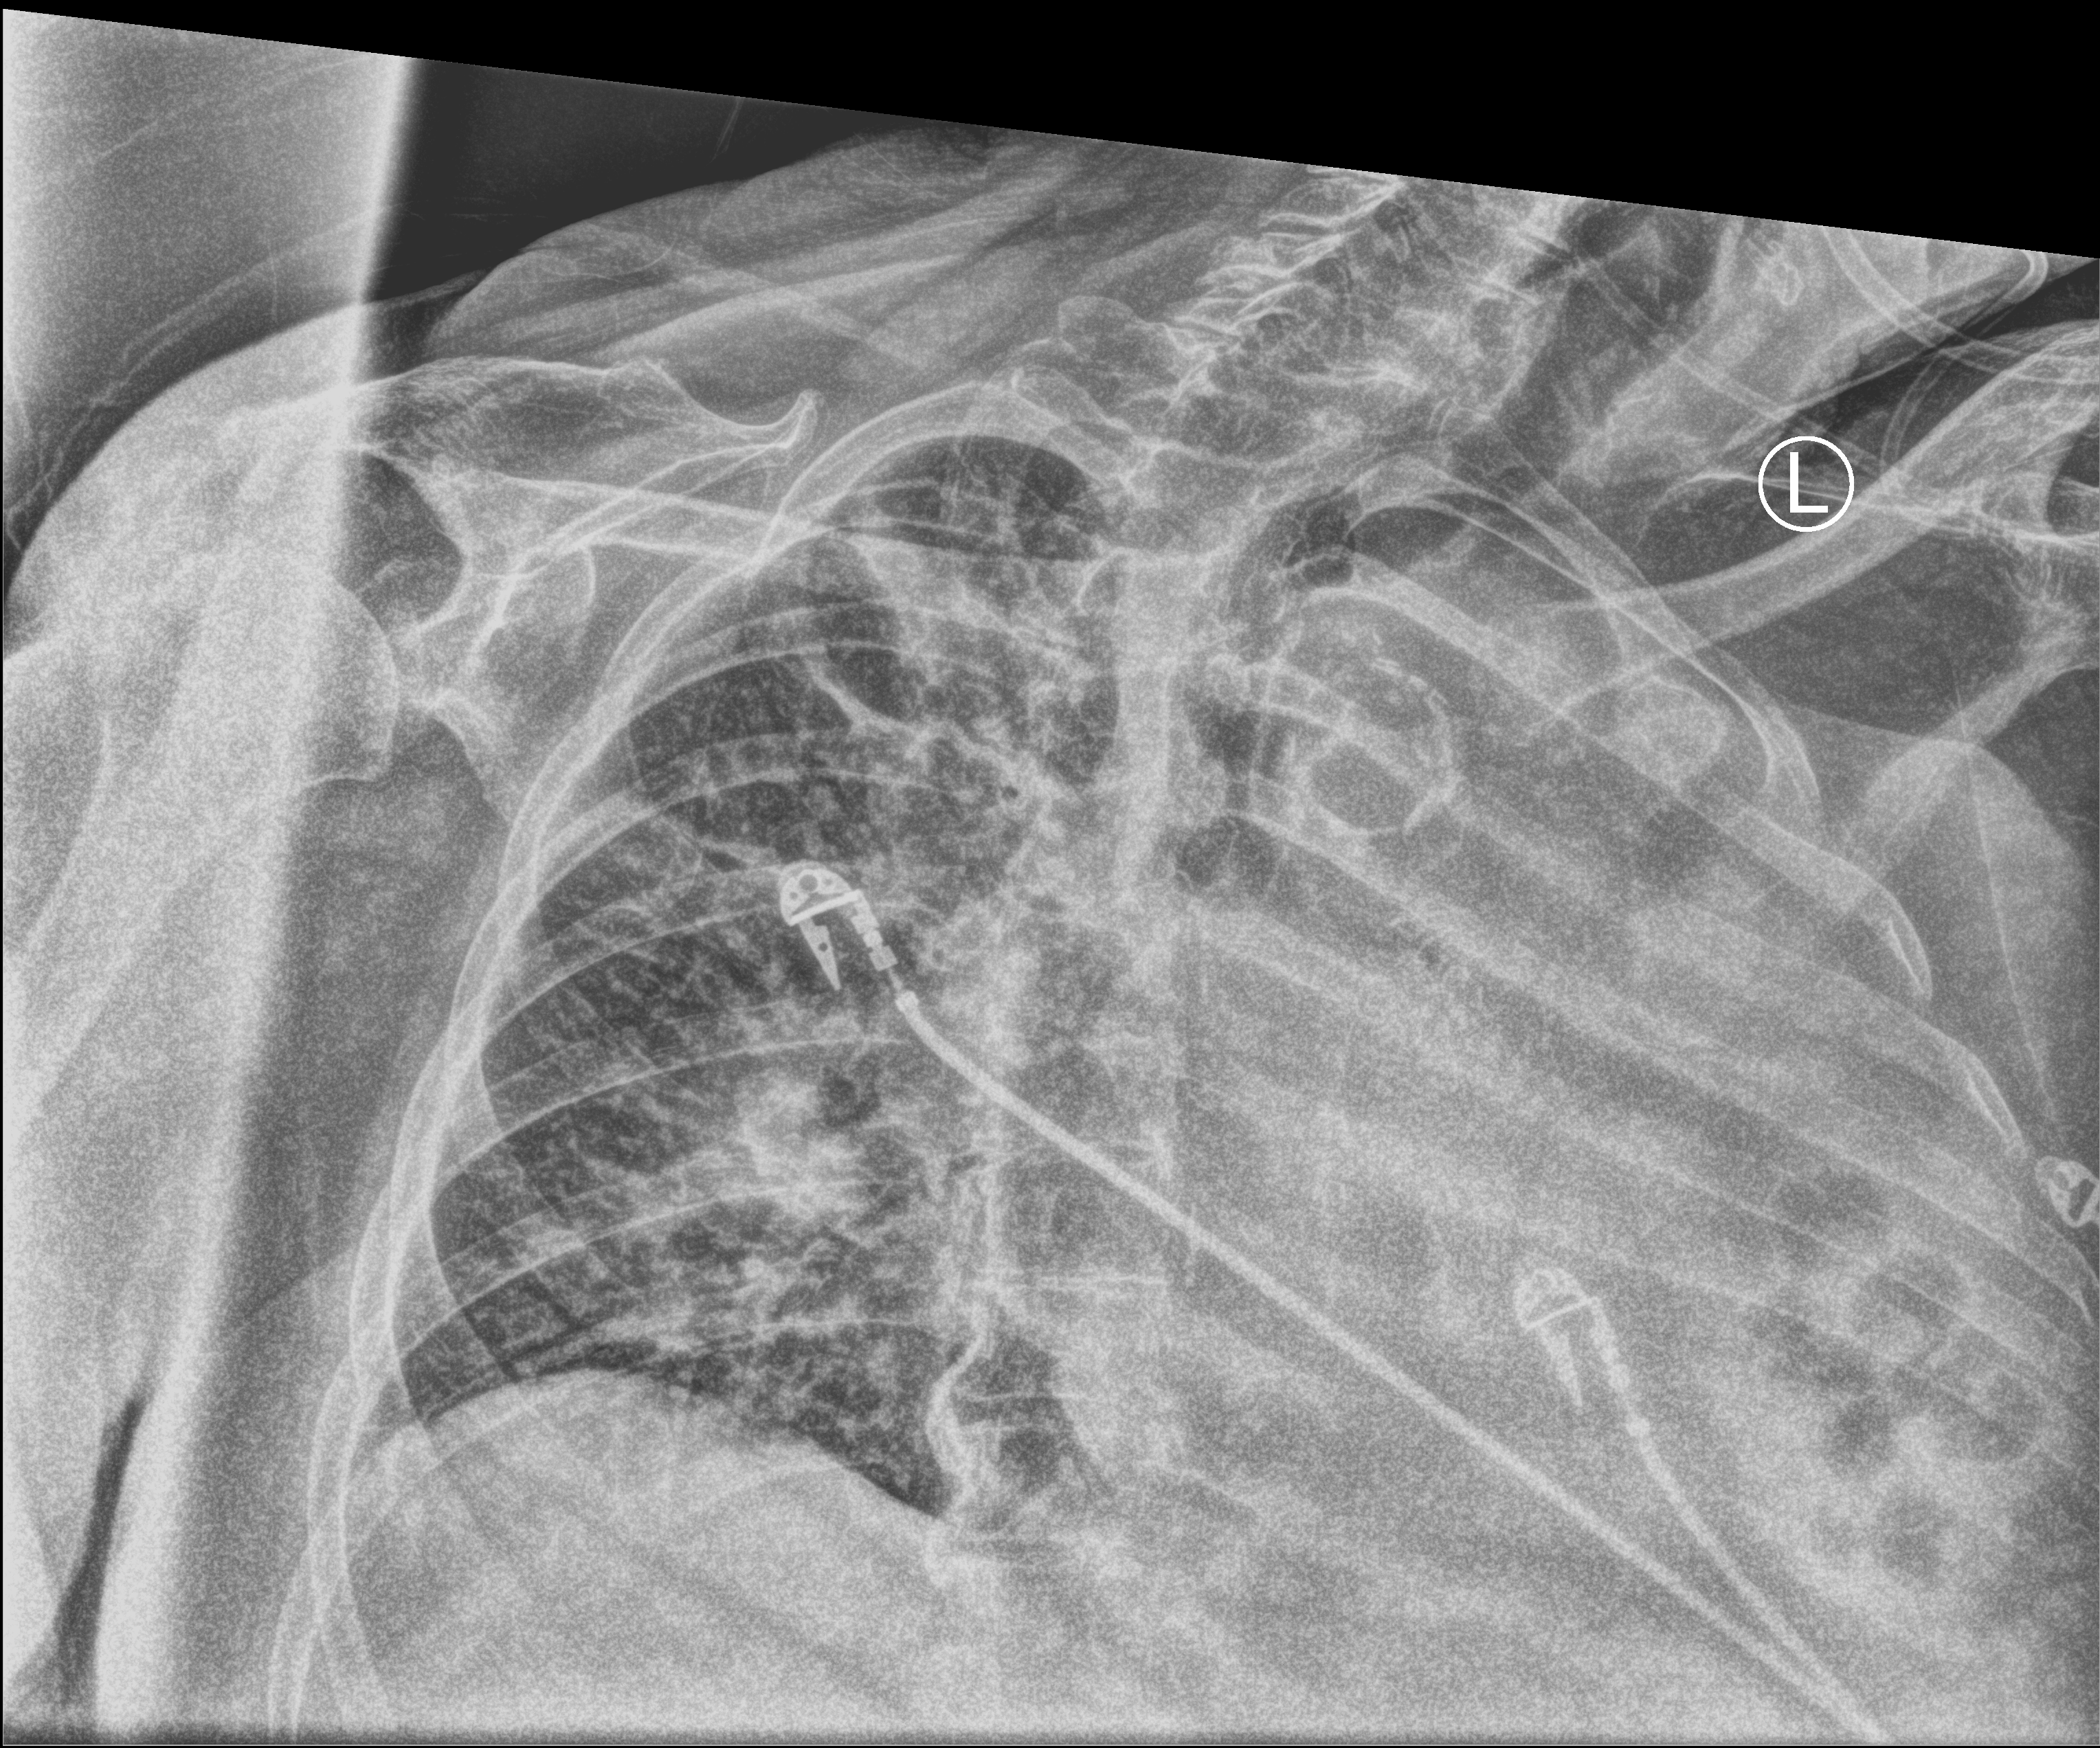
Bedside chest radiograph (computed radiography); anteroposterior (AP) projection. Female patient hospitalised with COVID-19, age 75–90 years.
Admission-level facts for this patient (not findings on this image; timing relative to this image not recorded): mechanically ventilated during this hospital stay: no; admitted to intensive care during this hospital stay: yes.